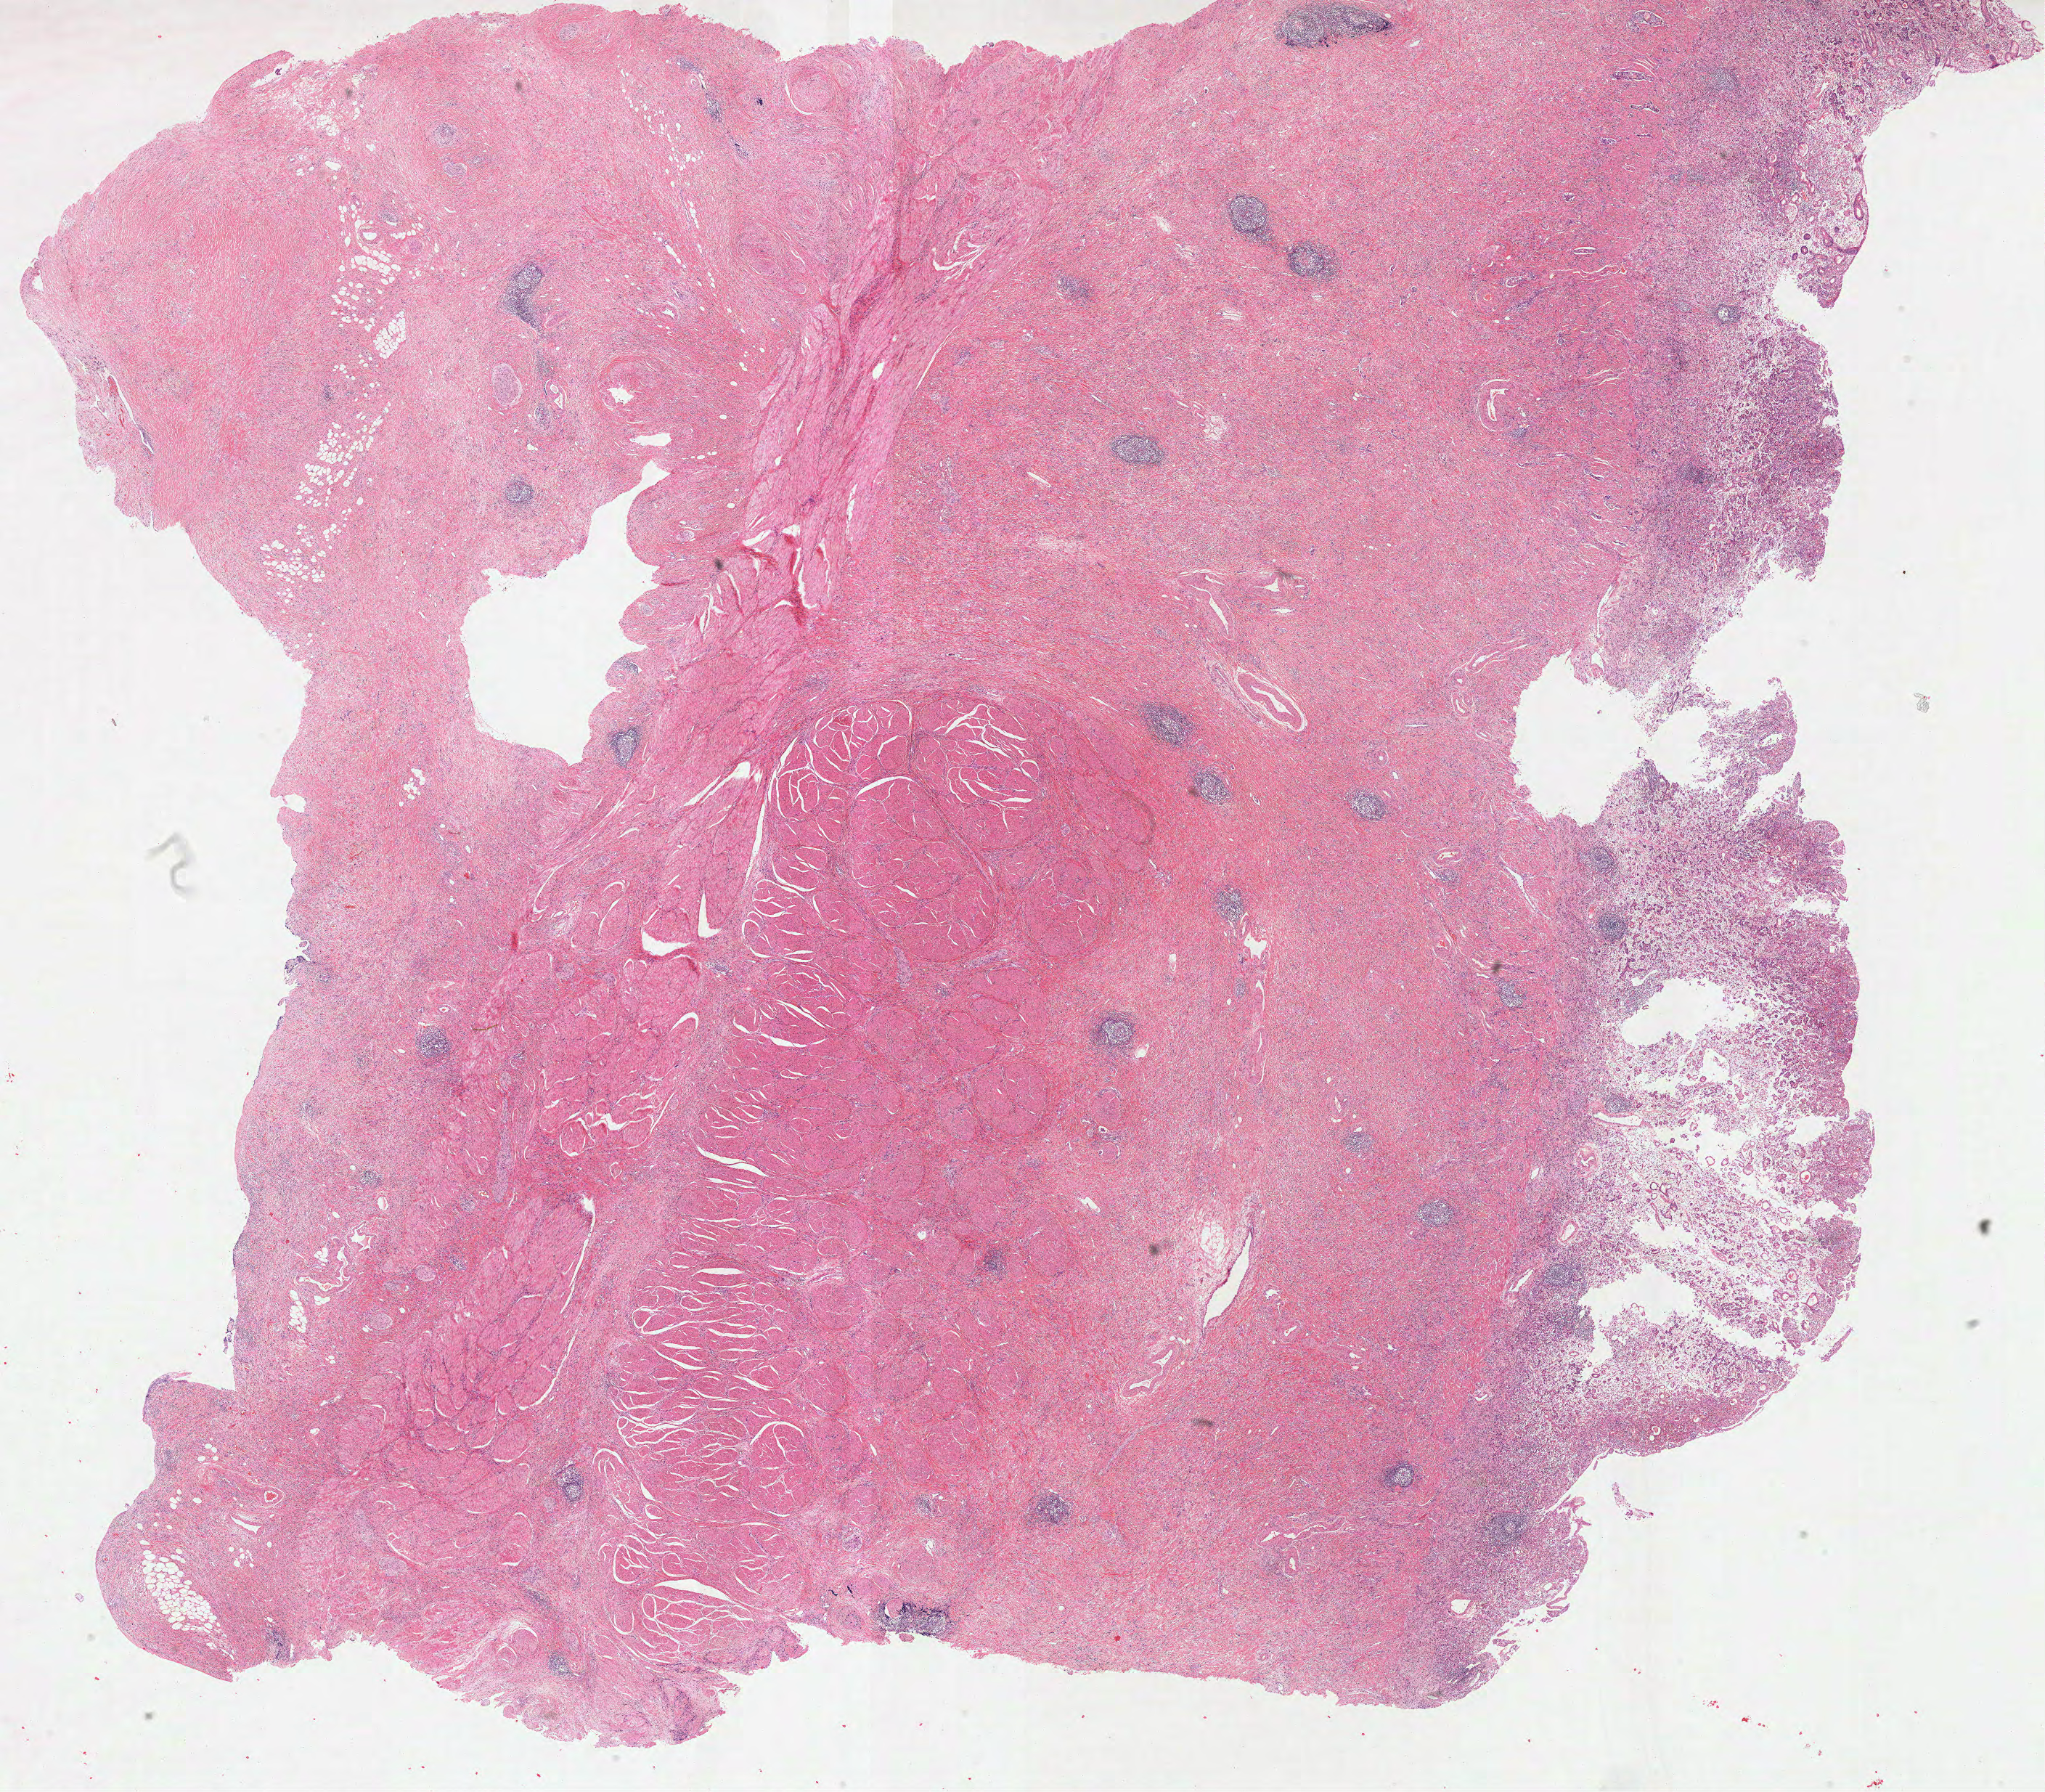
Whole-slide histology image, H&E, low-resolution overview of the scanned area, about 22.7 x 19.9 mm (acquisition: 40x scan), formalin-fixed paraffin-embedded (FFPE) diagnostic section, primary tumour sample from the stomach. Male patient; age at initial diagnosis 62 years. Histologic grade: G3 (poorly differentiated).
• pathologic diagnosis: Adenocarcinoma, NOS (cardia, NOS)
• AJCC pathologic stage: IIIB (7th edition)